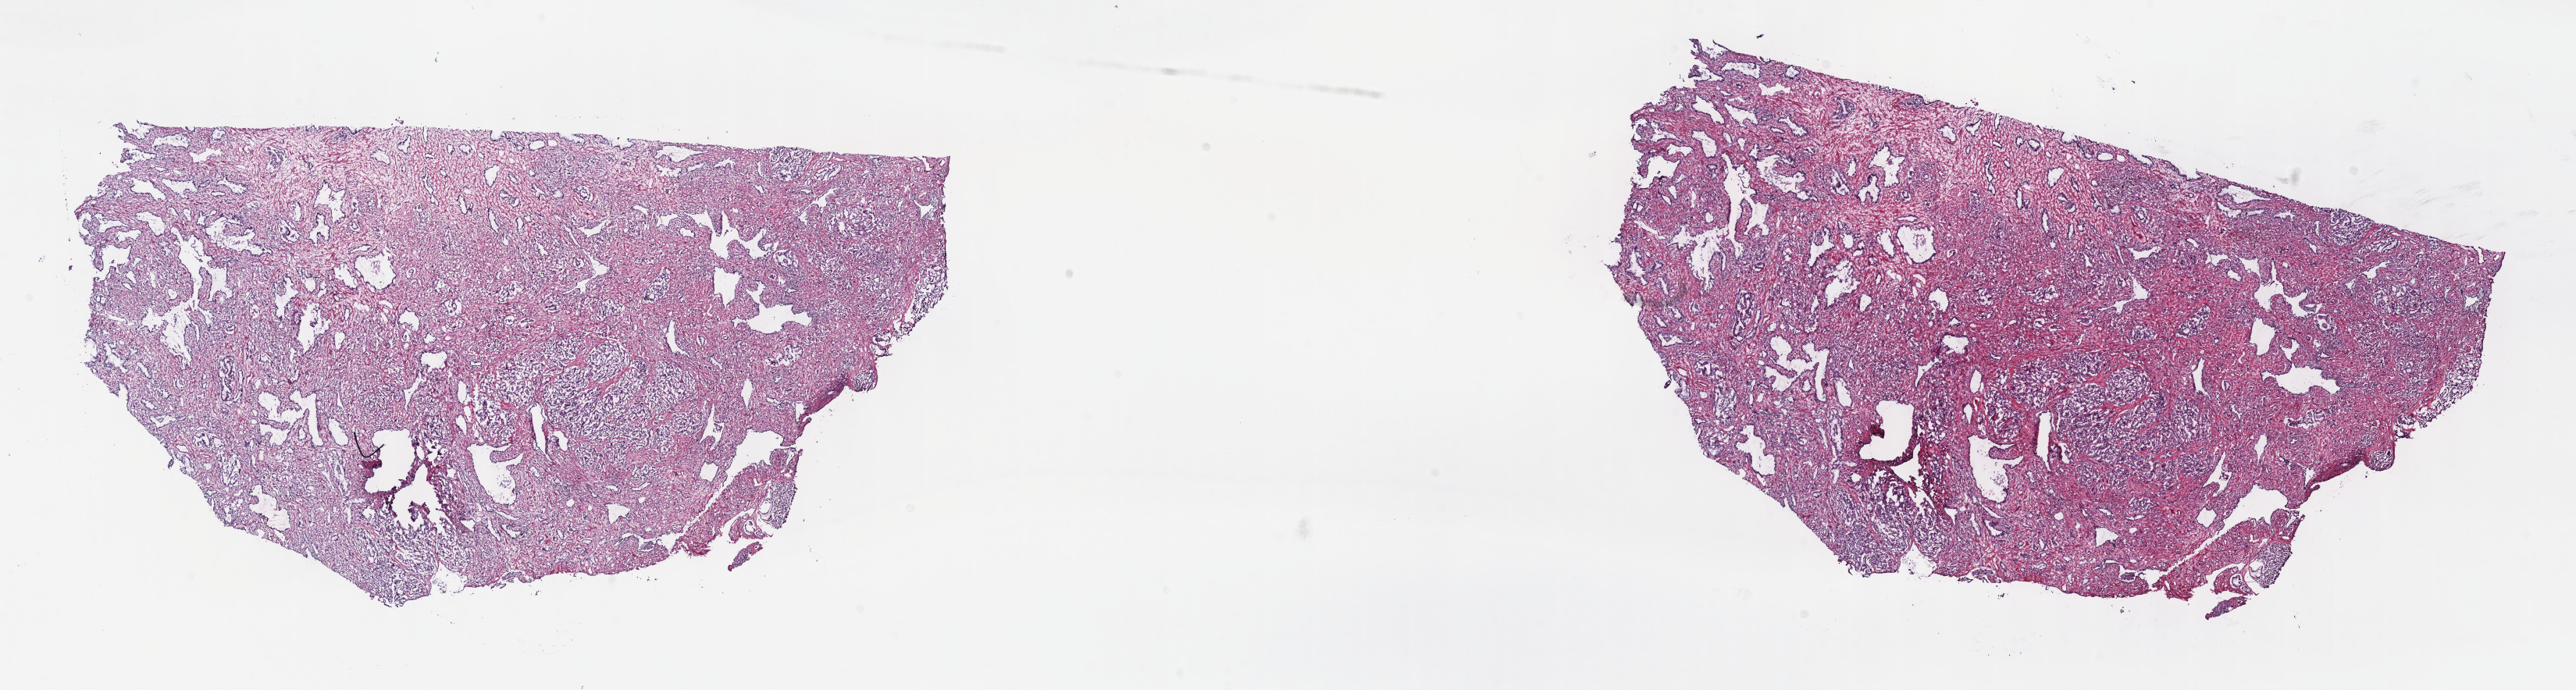
Digitized H&E tissue section (whole slide), low-resolution overview of the scanned area, about 26.7 x 7.1 mm (from a 40x scan); frozen section from the top of the tissue portion; primary tumour sample from the prostate. Male patient; age at initial diagnosis 55 years. Gleason score: 9 (4+5). Slide review estimates, as recorded: tumour cells 70%, tumour nuclei 70%, normal cells 10%, stromal cells 20%, necrosis 0%. Infiltration values recorded for this section: lymphocyte infiltration 40%, monocyte infiltration 20%, neutrophil infiltration 20%.
Diagnosis: Adenocarcinoma, NOS (prostate gland). Lymph nodes positive (case pathology): 0 of 9 examined. Laterality: bilateral.